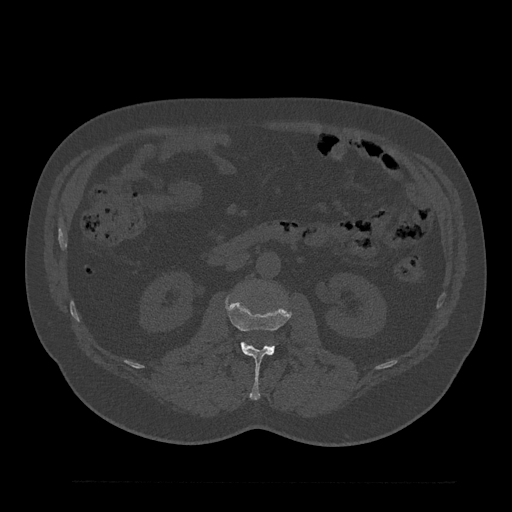
CT including the spine, one axial slice; slice 87 of 797 in the series (ordered by position); reconstruction kernel Br40s/3; 120 kVp; bone window (W 1800 / L 400 HU); 512 × 512 image matrix, field of view 430 × 430 mm. Male patient, age 61 years. Case-level facts recorded for this patient, not image findings: primary cancer: prostate.
Structures marked on this image (semi-automatic segmentation, software-assisted and operator-edited):
- L2 vertebra: bounding box (x1, y1, x2, y2) in pixels: (226, 297, 291, 400)